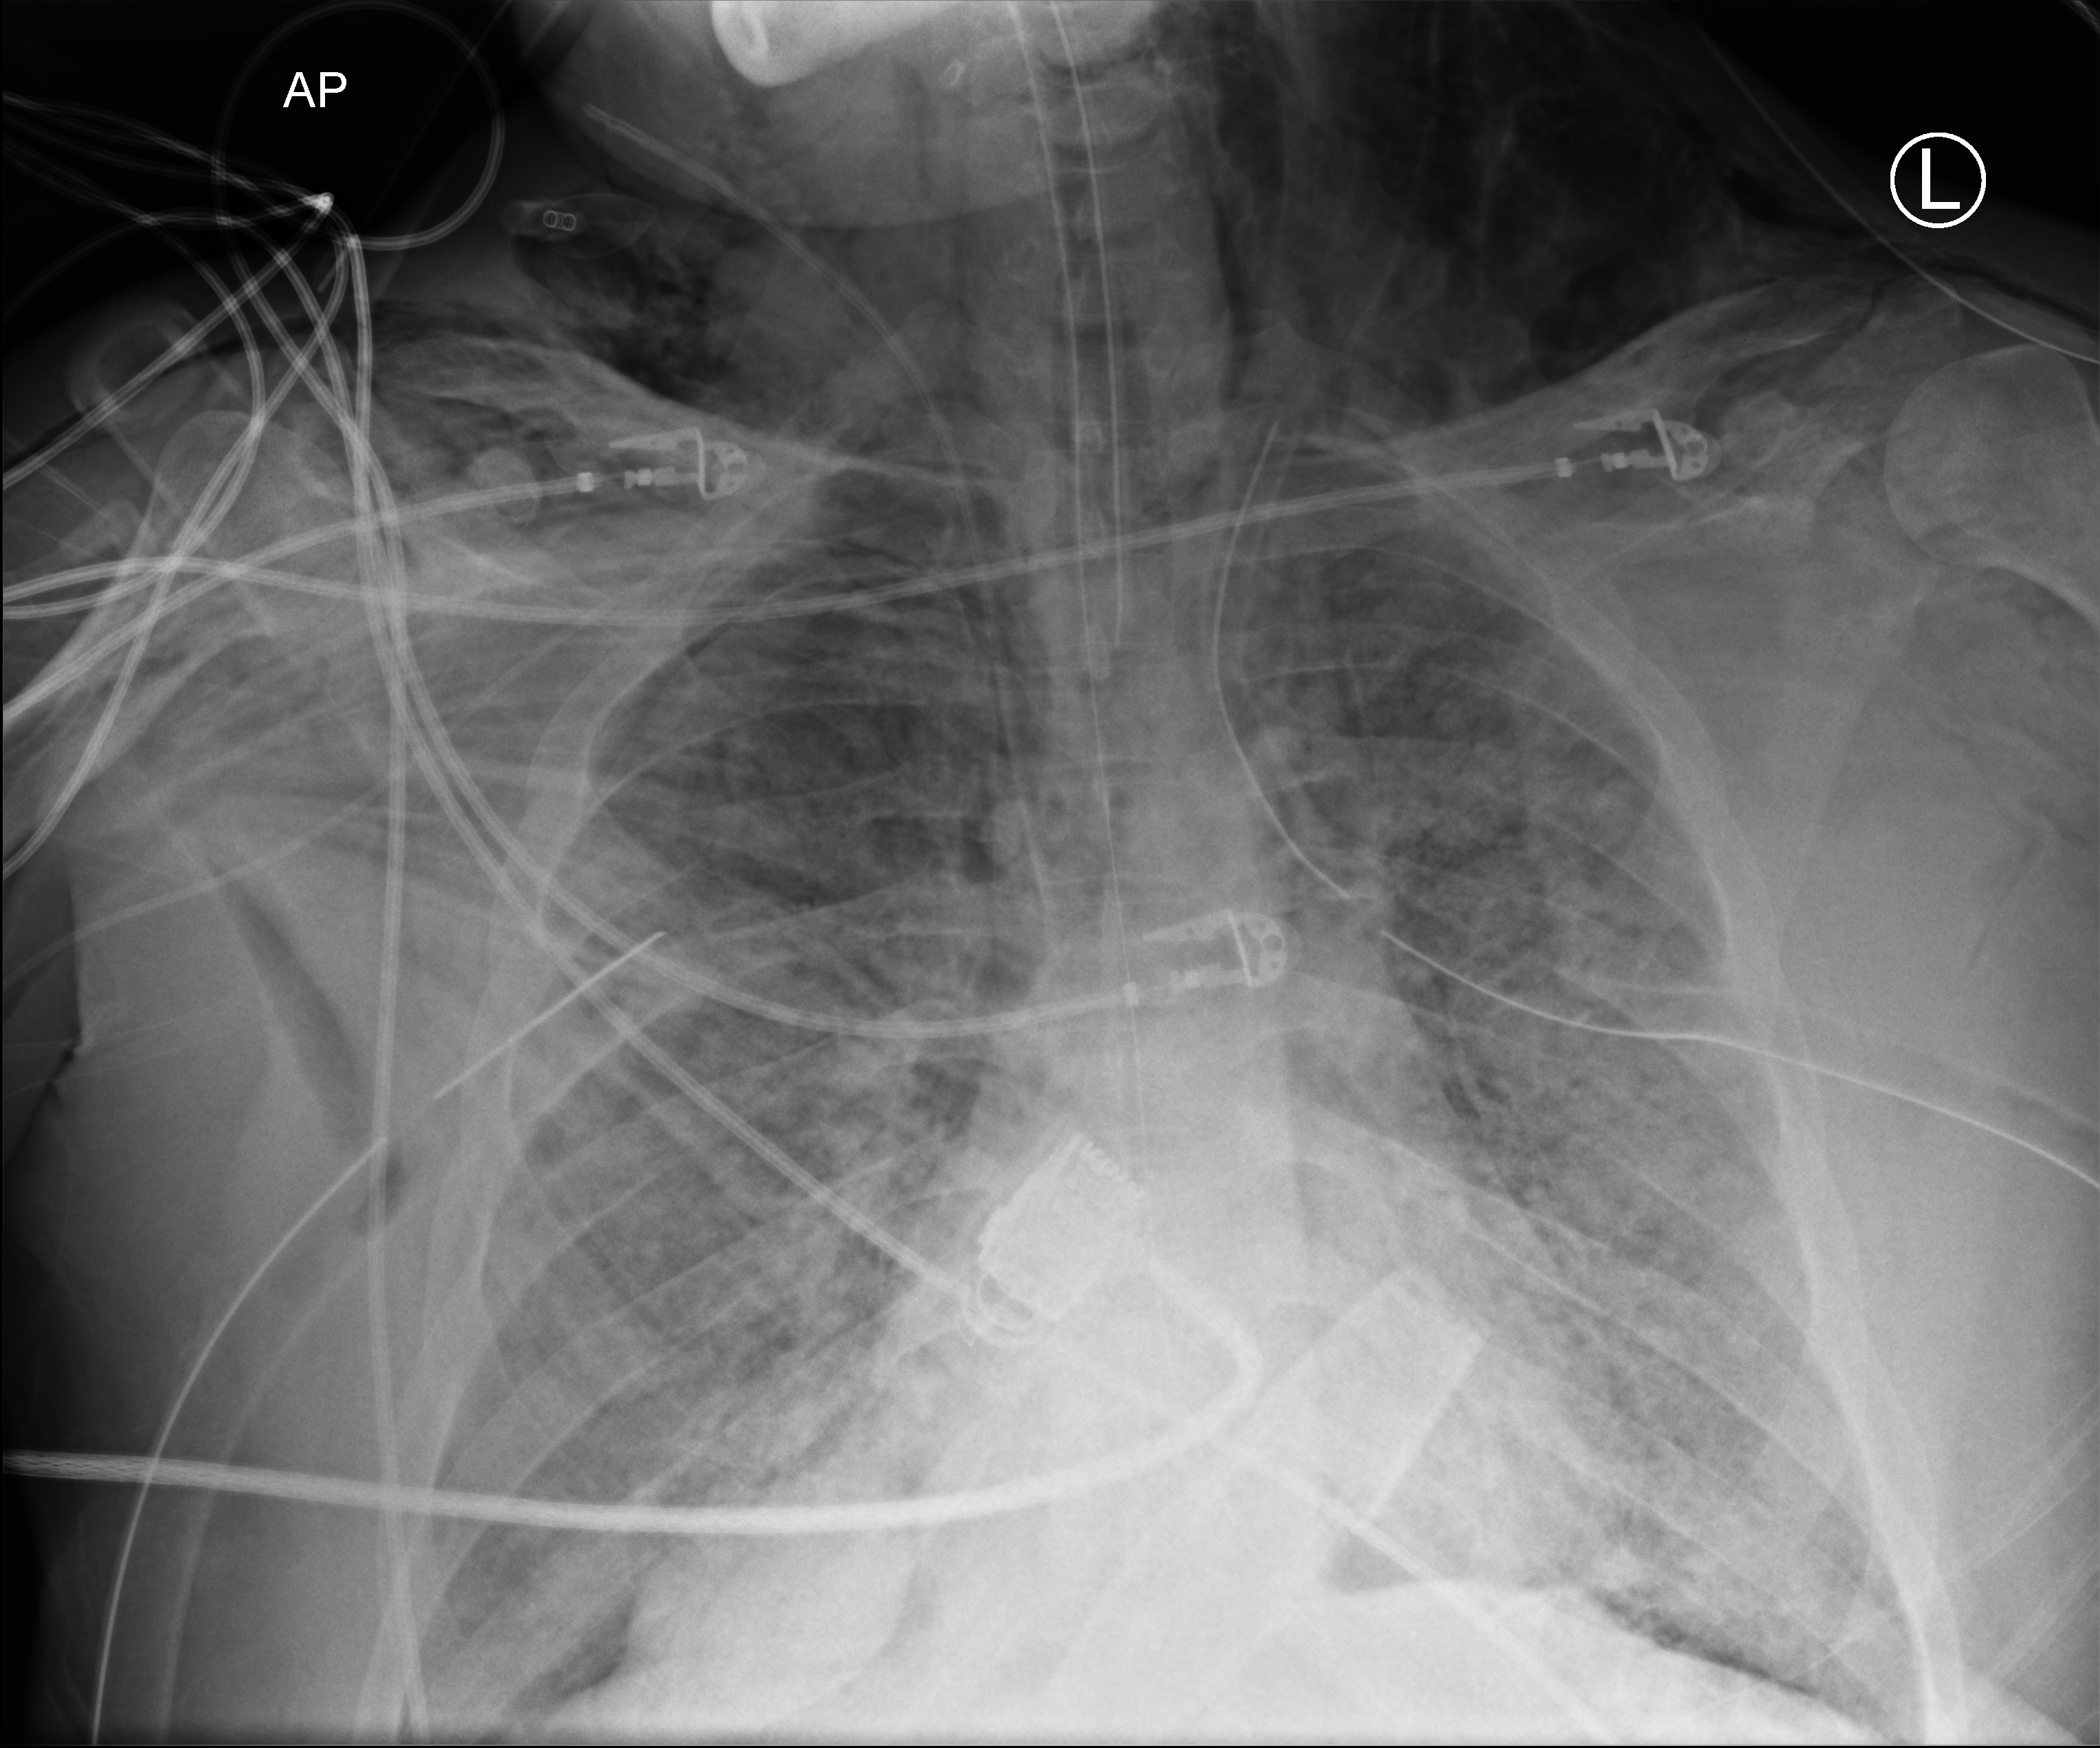
Bedside chest radiograph (computed radiography). Patient hospitalised with COVID-19, aged 18–59 years.
Hospital-stay facts (about this admission, not read from this image; timing relative to this image not recorded): other chronic lung disease (admission record): no.